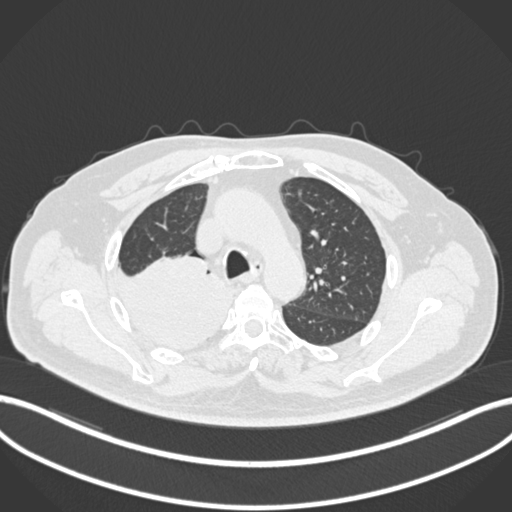
Chest CT, one axial slice. Position 150 of 218 along the scan axis. 120 kVp. Lung window (W 1500 / L -600 HU). 1 mm slice thickness. 512 × 512 image matrix, field of view 400 × 400 mm. Male patient, age 68 years. Case-level facts recorded for this patient, not image findings: clinical TNM (as recorded): T2a N0 M0.
Structures marked on this image (bounding box drawn by a radiologist):
- lung tumour (recorded histology: adenocarcinoma): bounding box (x1, y1, x2, y2) in pixels: (109, 253, 234, 358)